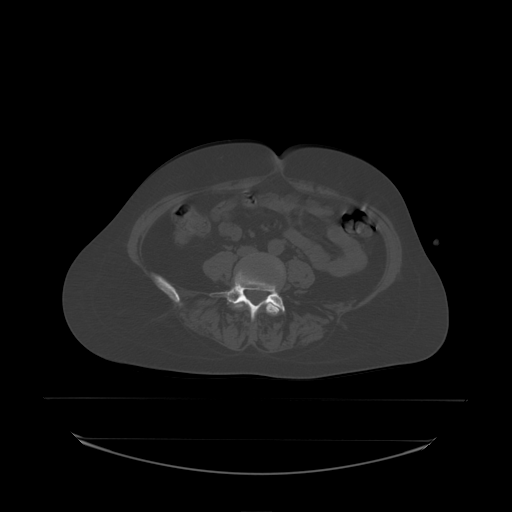
CT including the spine, one axial slice. Slice 43 of 242 in the series (ordered by position). Bone window (W 1800 / L 400 HU). 512 × 512 image matrix, field of view 500 × 500 mm. Female patient, age 53 years. From the clinical record (not read from this slice): primary cancer: lung; vertebrae with lytic lesions (as recorded): T7, L1.
Annotated regions visible in this slice (semi-automatic segmentation, software-assisted and operator-edited):
- L4 vertebra: bounding box <235,265,282,316> (left, top, right, bottom; pixels)
- L5 vertebra: <214,270,286,320>